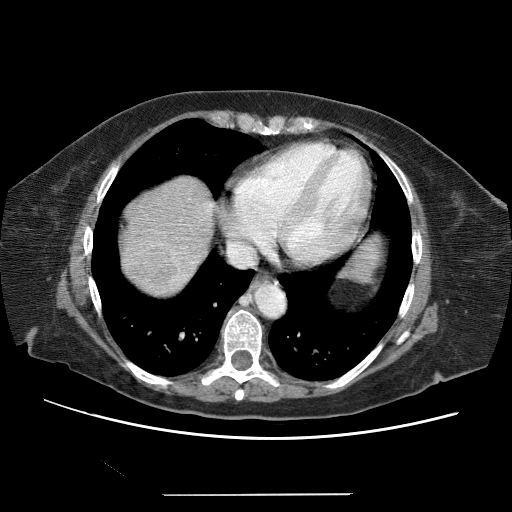
Contrast-enhanced abdominal CT (liver protocol), one axial slice; position 59 of 65 along the scan axis; reconstruction kernel STANDARD; soft-tissue window (W 400 / L 40 HU); 2.5 mm slice thickness; 512 × 512 image matrix, field of view 380 × 380 mm. Case-level facts recorded for this patient, not image findings: diagnosis: hepatocellular carcinoma (patient treated with transarterial chemoembolisation; whether this scan precedes or follows treatment is not stated here); TNM stage (as recorded): Stage-IIIB; Child-Pugh class: A; tumour differentiation: moderately differentiated; tumour nodularity: uninodular.
Outlined on this slice (semi-automatic segmentation, software-assisted and operator-edited):
- abdominal aorta: bounding box (x1, y1, x2, y2) in pixels: (257, 284, 286, 318)
- liver parenchyma outside the tumour (the mass and vessels are separate outlines, so this box may not span the whole liver): (128, 182, 212, 286)
- mass: (134, 238, 188, 288)
- liver vessels: (141, 204, 210, 256)